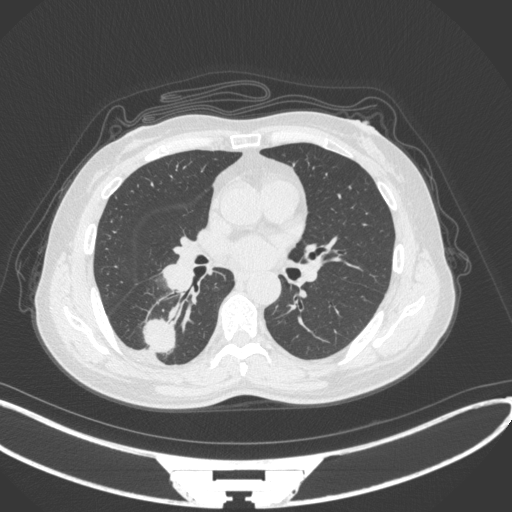
Chest CT, one axial slice. Position 158 of 352 along the scan axis. Lung window (W 1500 / L -600 HU). 1 mm slice thickness. 512 × 512 image matrix. Female patient, age 55 years. Case-level facts recorded for this patient, not image findings: clinical TNM (as recorded): T1c N1 M0.
Structures marked on this image (rectangle marked by the reading radiologist):
- lung tumour (recorded histology: adenocarcinoma): bounding box (x1, y1, x2, y2) in pixels: (140, 314, 183, 356)